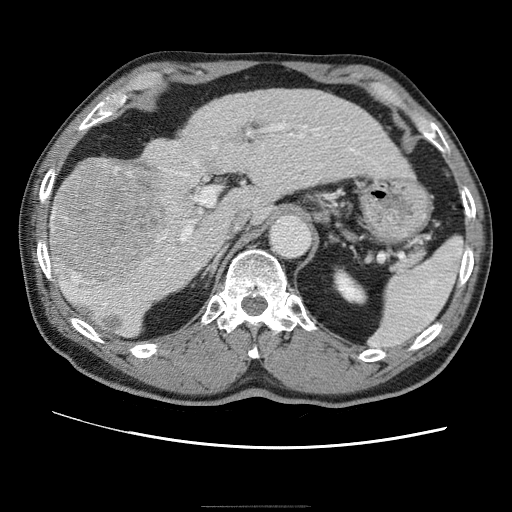
Contrast-enhanced abdominal CT (liver protocol), one axial slice; position 34 of 75 along the scan axis; reconstruction kernel STANDARD; one of 2 acquisitions stored at this slice position; soft-tissue window (W 400 / L 40 HU); 2.5 mm slice thickness; 512 × 512 image matrix, field of view 360 × 360 mm. From the clinical record (not read from this slice): diagnosis: hepatocellular carcinoma (patient treated with transarterial chemoembolisation; whether this scan precedes or follows treatment is not stated here); TNM stage (as recorded): Stage-II; Child-Pugh class: A; tumour differentiation: well differentiated; tumour nodularity: multinodular.
Outlined on this slice (semi-automatic segmentation, software-assisted and operator-edited):
- liver parenchyma outside the tumour (the mass and vessels are separate outlines, so this box may not span the whole liver): bounding box [x1, y1, x2, y2] px = [51, 90, 406, 336]
- mass: [53, 166, 166, 296]
- liver vessels: [60, 120, 335, 306]